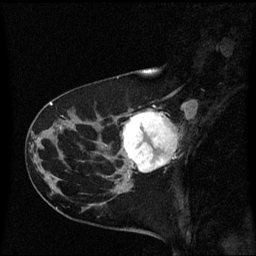
Breast MRI (dynamic contrast-enhanced), one sagittal slice; position 23 of 60 along the scan axis; dynamic contrast-enhanced series, image 2 of 3 at this slice position (ordered by acquisition); 1.5 T; TE 4.2 ms, TR 8.4 ms; 2 mm slice thickness; 256 × 256 image matrix. Female patient, age 41 years. From the clinical record (not read from this slice): setting: breast cancer imaged before/during neoadjuvant chemotherapy; receptor status: triple-negative.
Outlined on this slice (semi-automatically segmented with operator editing):
- analysis volume of interest (the breast-tissue region the enhancement analysis was run in; not a lesion): bounding box <116,110,178,177> (left, top, right, bottom; pixels)
- tumour enhancement mask (voxels above the 70 % enhancement threshold inside the analysis volume of interest): <122,110,178,177>